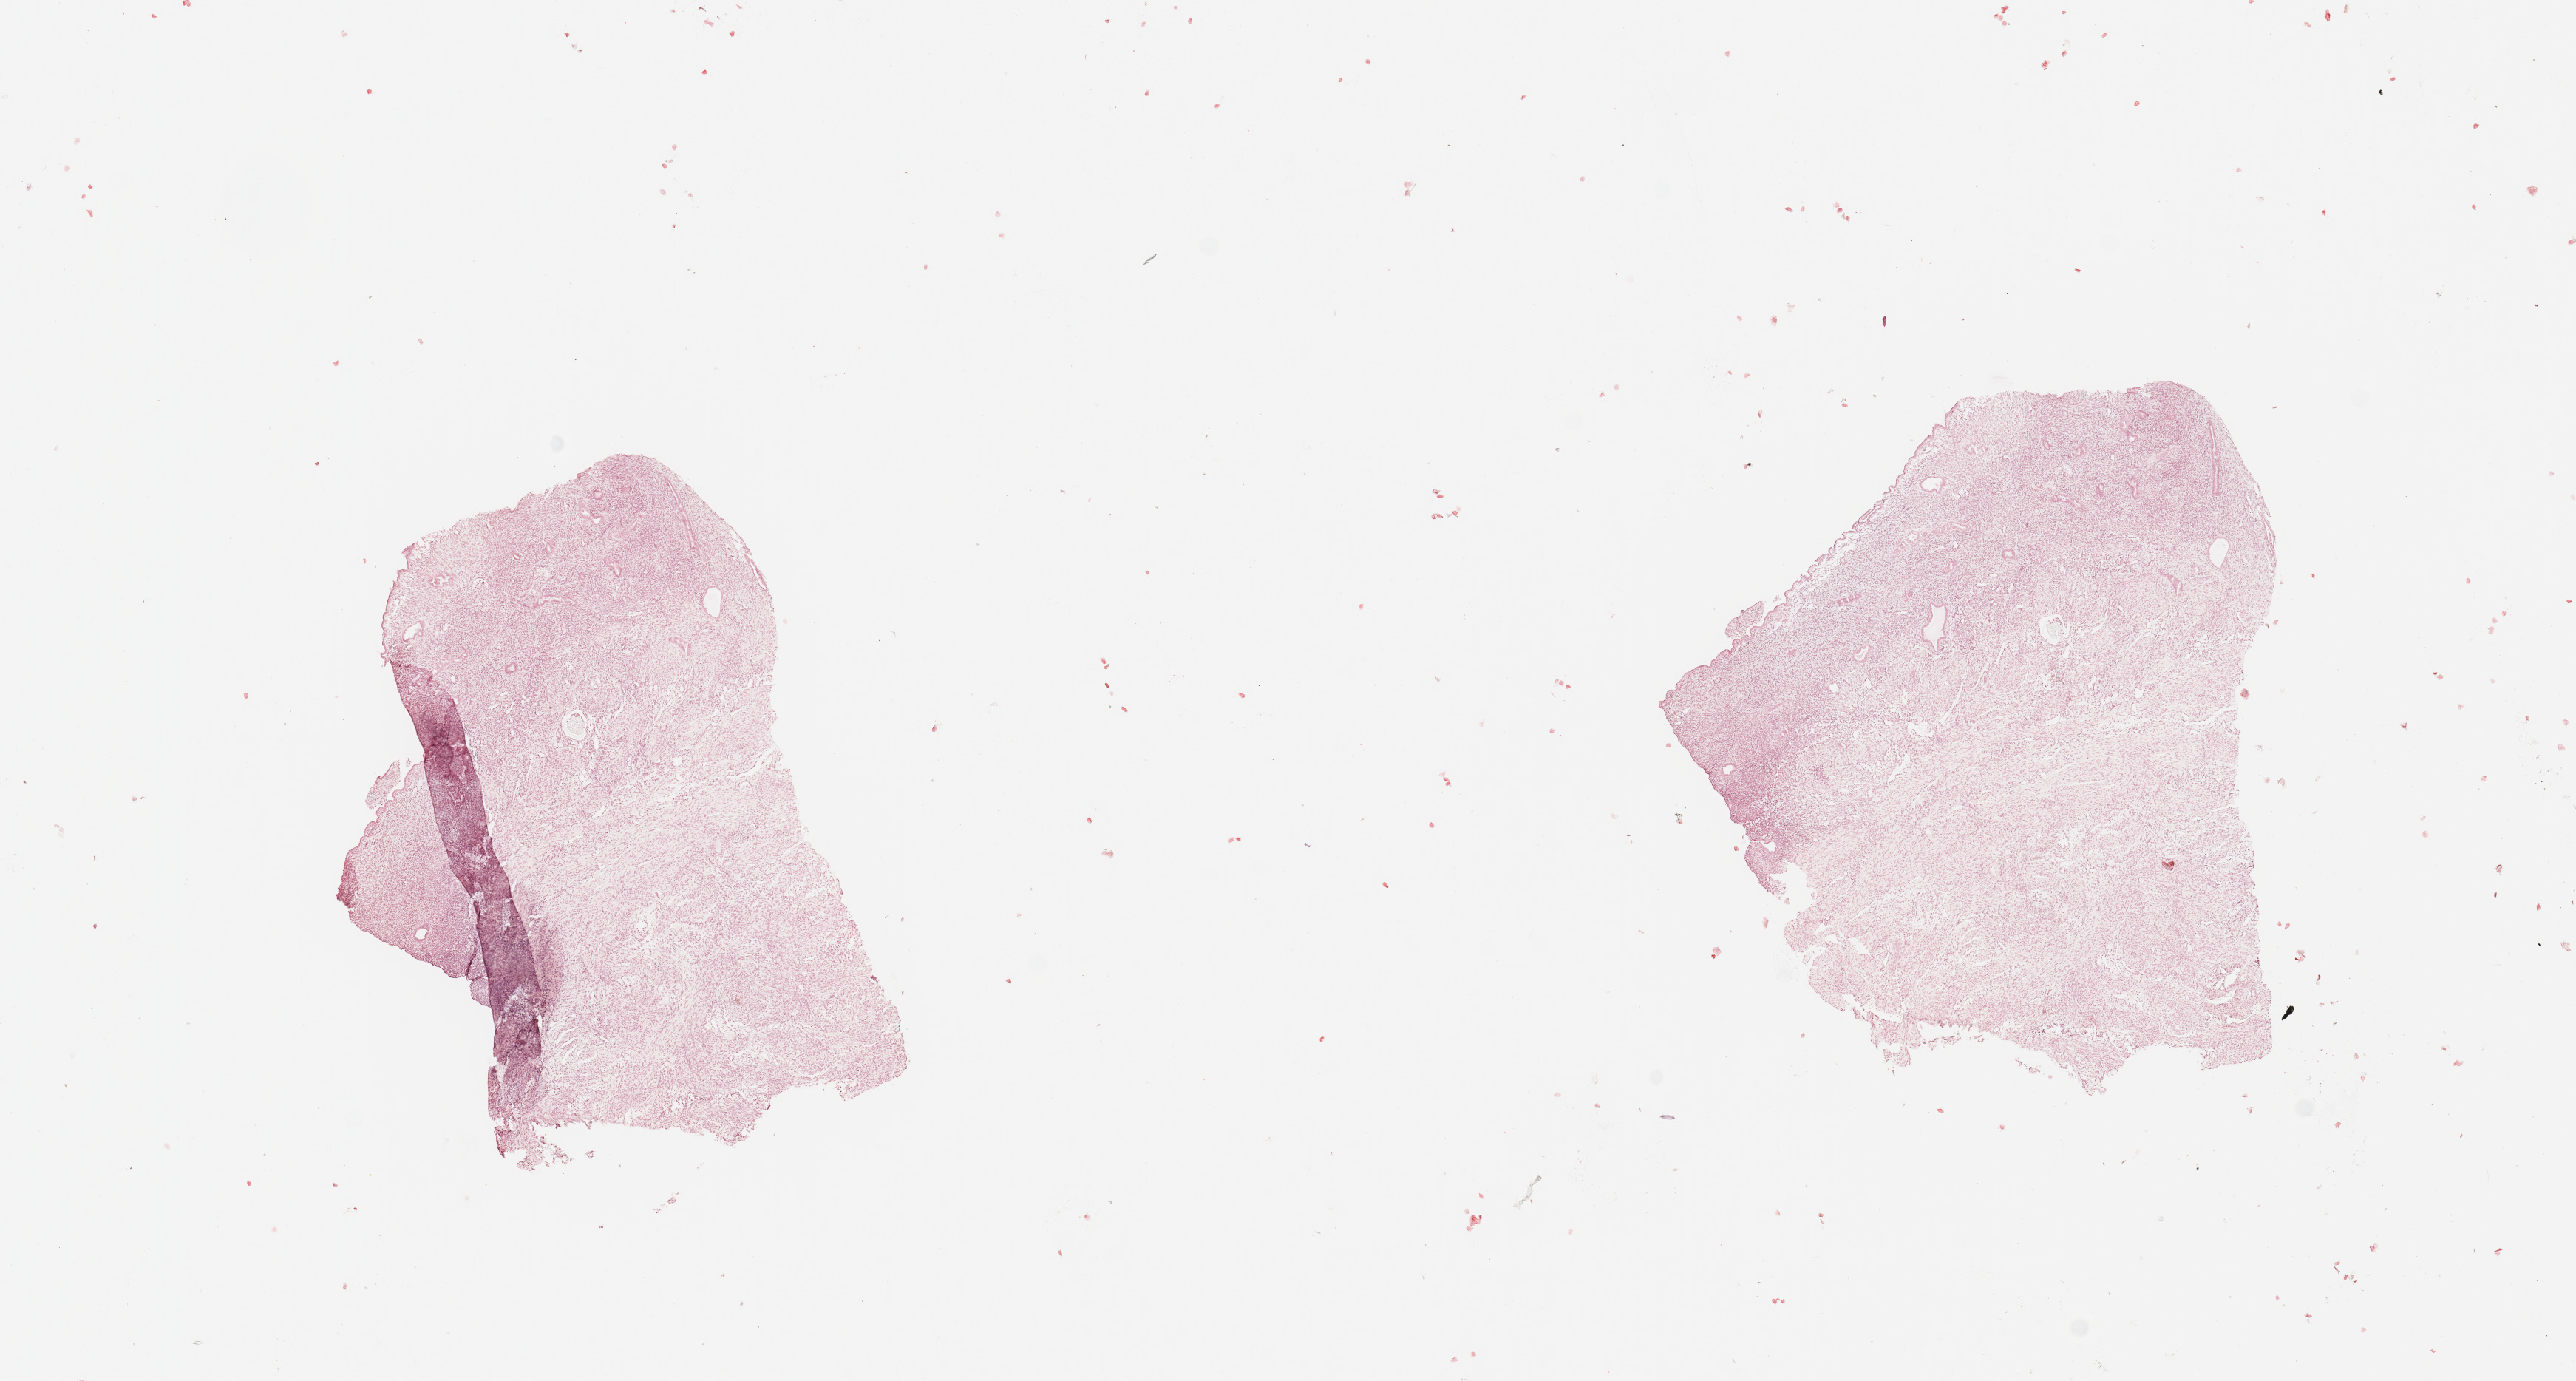
Digitized H&E tissue section (whole slide) — low-resolution overview of the scanned area, about 13.8 x 7.4 mm (acquisition: 20x scan). Female, 59 y/o.
Patient diagnosis (cohort enrolment): sarcoma (site not recorded at cohort level). Primary tumour site (as recorded): gynecologic.